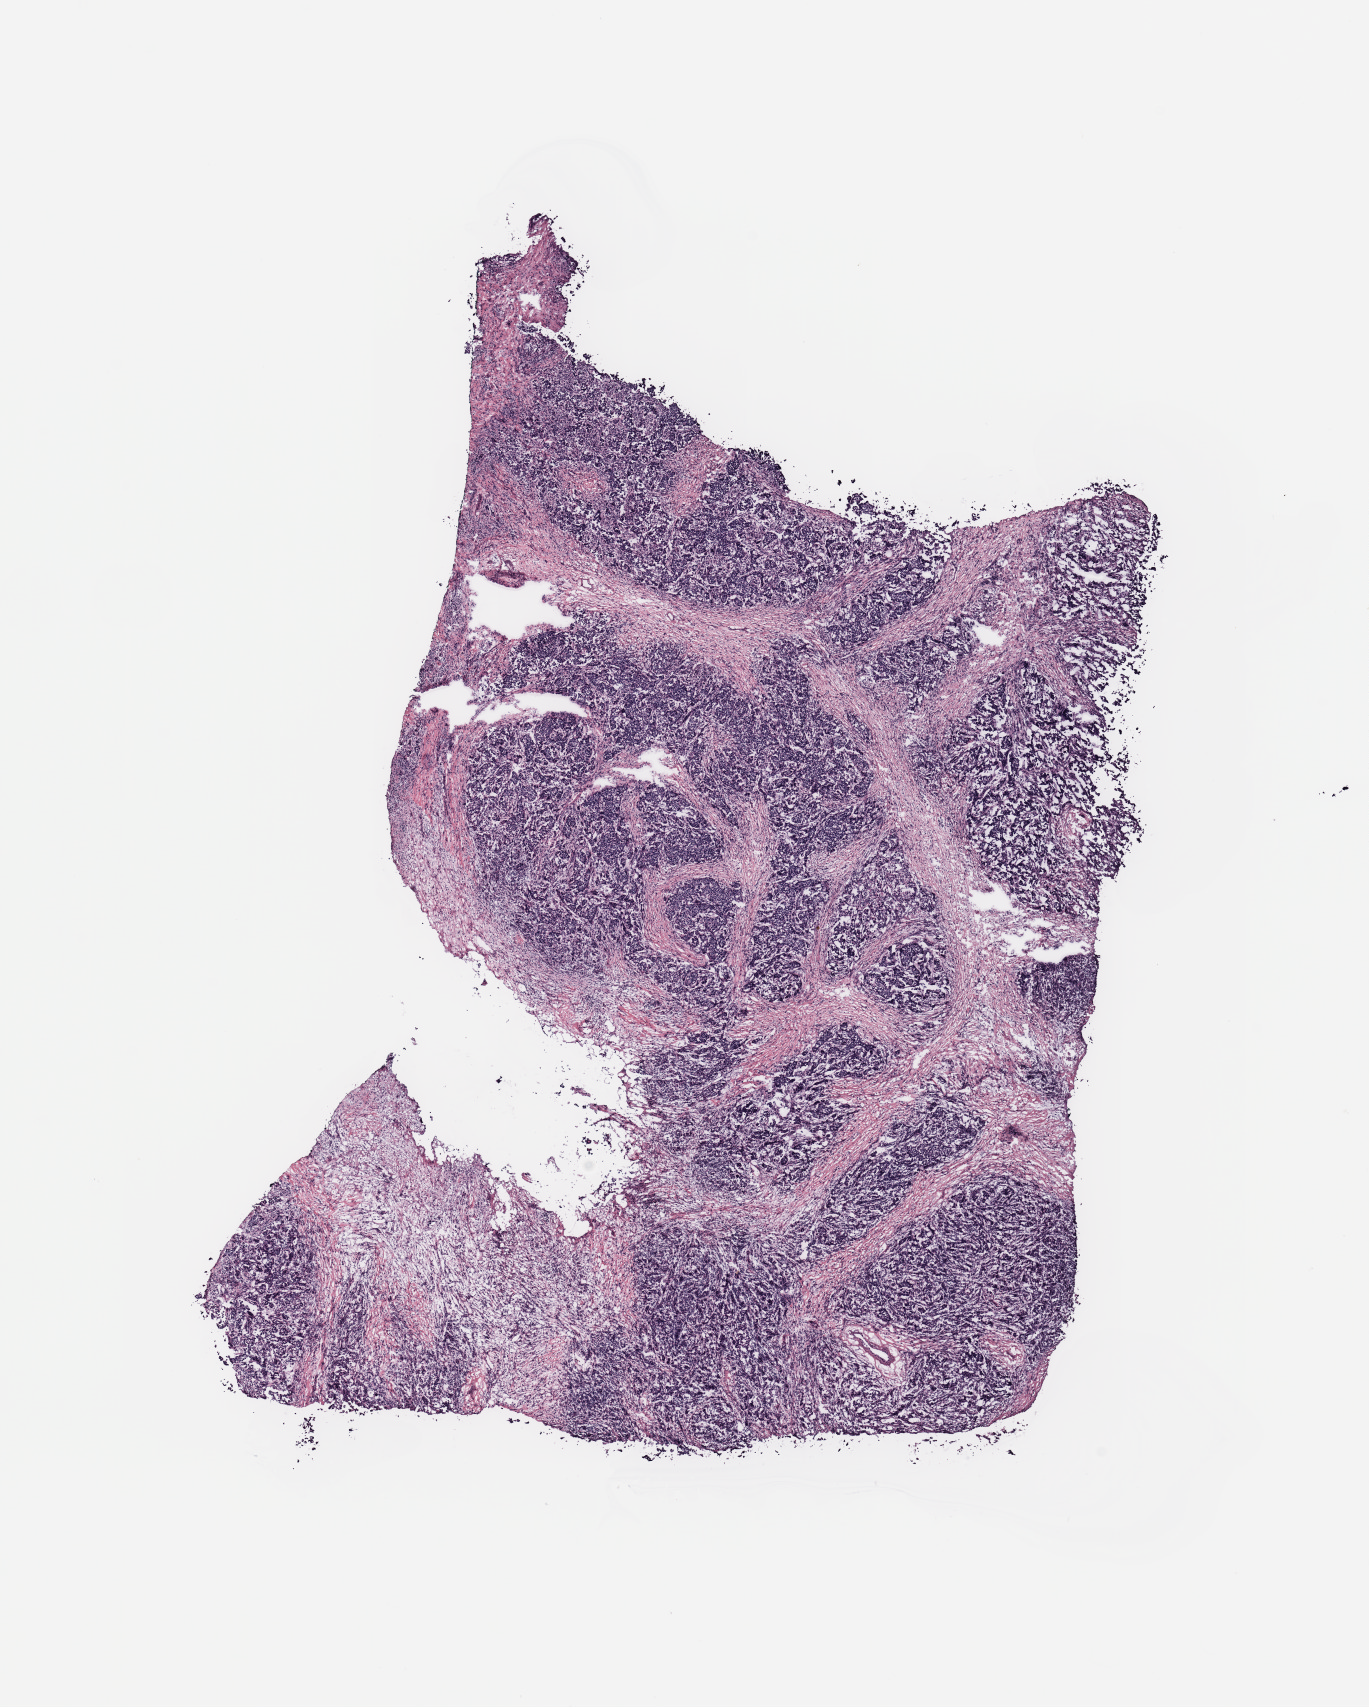
Digitized H&E tissue section (whole slide) — low-resolution overview of the scanned area, about 10.8 x 13.5 mm (acquisition: 20x scan). Female, 86 y/o.
Specimen: breast, tumour tissue.